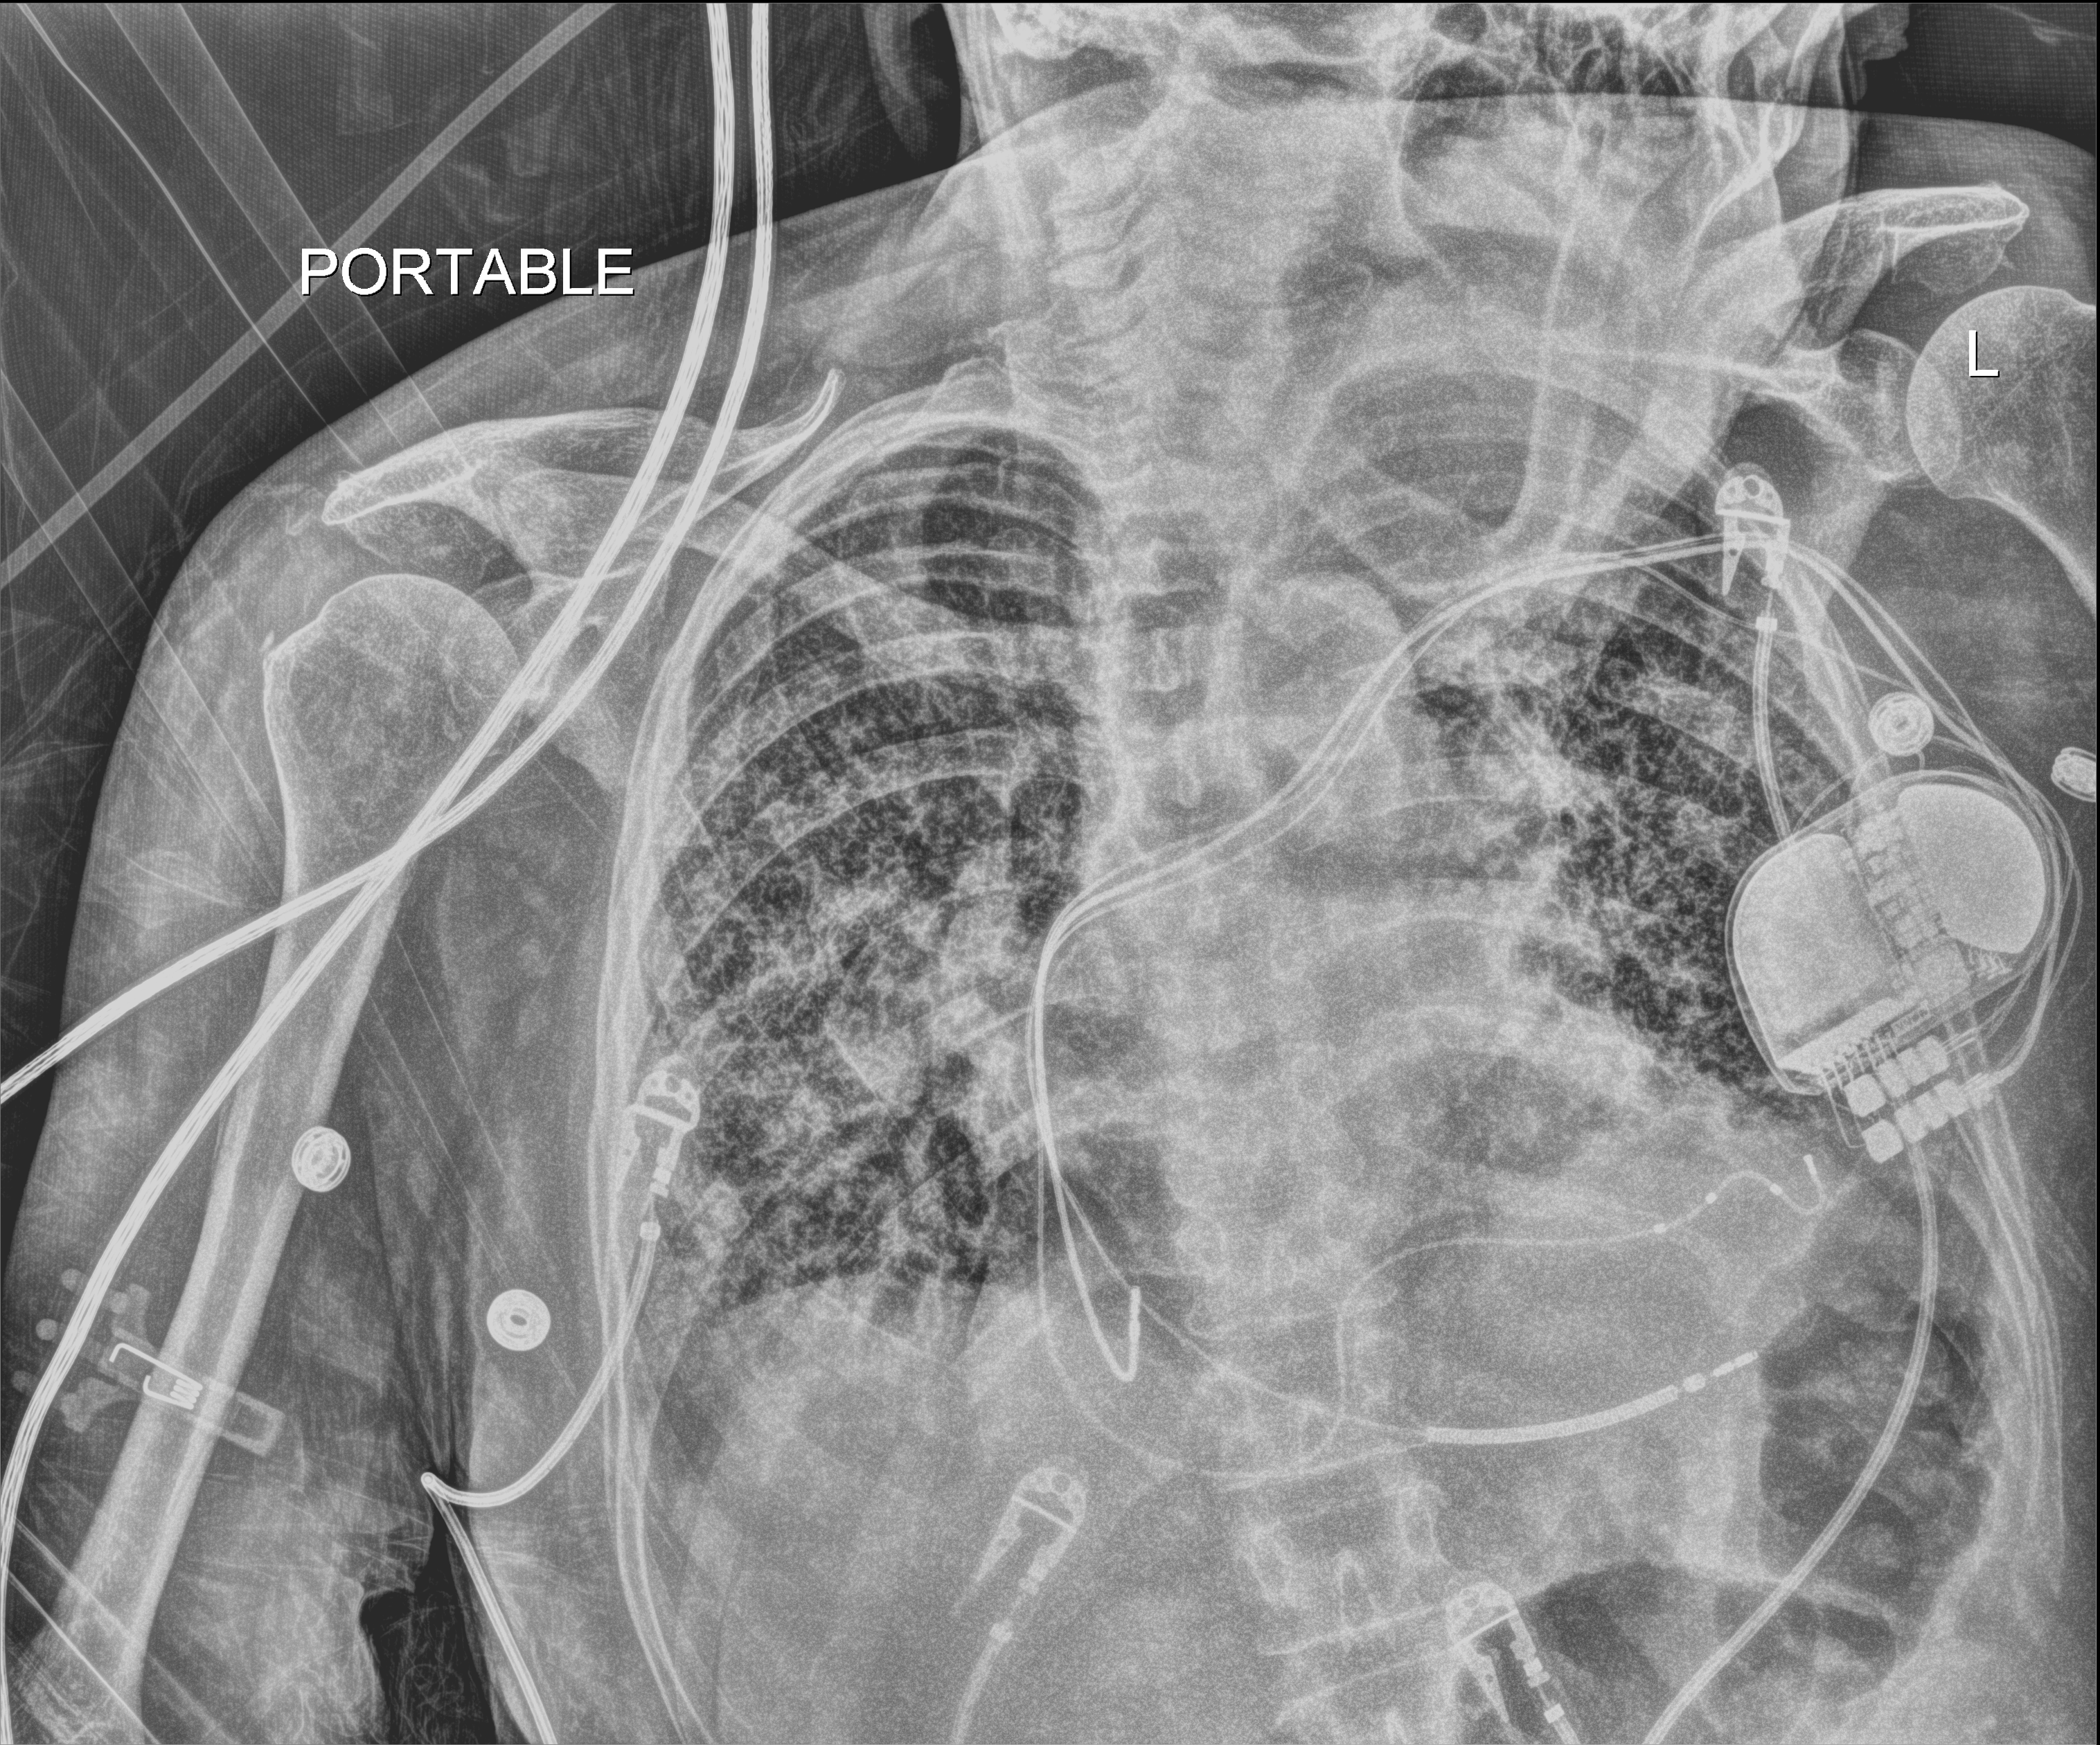
Chest X-ray (portable); anteroposterior (AP) projection. Patient hospitalised with COVID-19; female, aged 60–74 years.
Admission-level facts for this patient (not findings on this image; timing relative to this image not recorded): length of hospital stay: 6 days; admitted to intensive care during this hospital stay: yes; mechanically ventilated during this hospital stay: no.